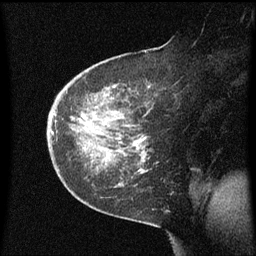
Breast MRI (dynamic contrast-enhanced), one sagittal slice; slice 38 of 60 in the series (ordered by position); dynamic contrast-enhanced series, image 2 of 3 at this slice position (ordered by acquisition); 1.5 T; TE 4.2 ms, TR 8.4 ms; 2 mm slice thickness; 256 × 256 image matrix, field of view 200 × 200 mm. Female patient, age 38 years. From the clinical record (not read from this slice): setting: breast cancer imaged before/during neoadjuvant chemotherapy; receptor status: HER2-positive.
Structures marked on this image (semi-automatic segmentation, software-assisted and operator-edited):
- analysis volume of interest (the breast-tissue region the enhancement analysis was run in; not a lesion): box from (x=47, y=50) to (x=160, y=185) px
- tumour enhancement mask (voxels above the 70 % enhancement threshold inside the analysis volume of interest): (x=136, y=138)–(x=145, y=141)